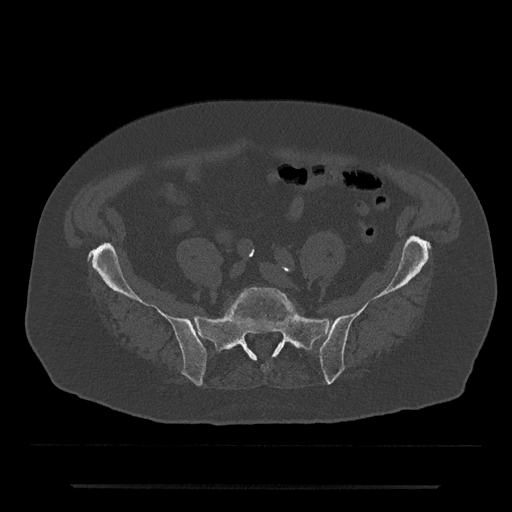
CT including the spine, one axial slice. Position 250 of 797 along the scan axis. Reconstruction kernel Br40s/3. Bone window (W 1800 / L 400 HU). 0.5 mm slice thickness. 512 × 512 image matrix, field of view 434 × 434 mm. Patient: male, 80 years. From the clinical record (not read from this slice): primary cancer: prostate.
Outlined on this slice (semi-automatically segmented with operator editing):
- L5 vertebra: bounding box [x1, y1, x2, y2] px = [226, 287, 299, 349]